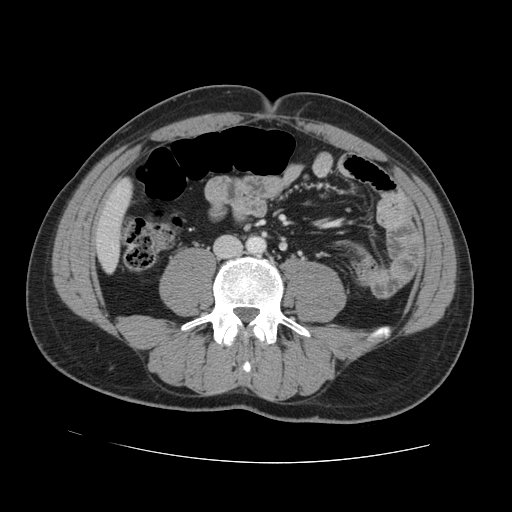
Contrast-enhanced abdominal CT, one axial slice. Slice 14 of 131 in the series (ordered by position). 120 kVp. Intravenous contrast given. Soft-tissue window (W 400 / L 40 HU). 2.5 mm slice thickness. 512 × 512 image matrix. Male patient, age 40 years. Case-level facts recorded for this patient, not image findings: diagnosis: colorectal cancer liver metastases, imaged before liver resection; multiple liver metastases: yes; largest metastasis: 2.9 cm.
Annotated regions visible in this slice (manually delineated by an expert):
- liver: bounding box [x1, y1, x2, y2] px = [97, 183, 131, 270]